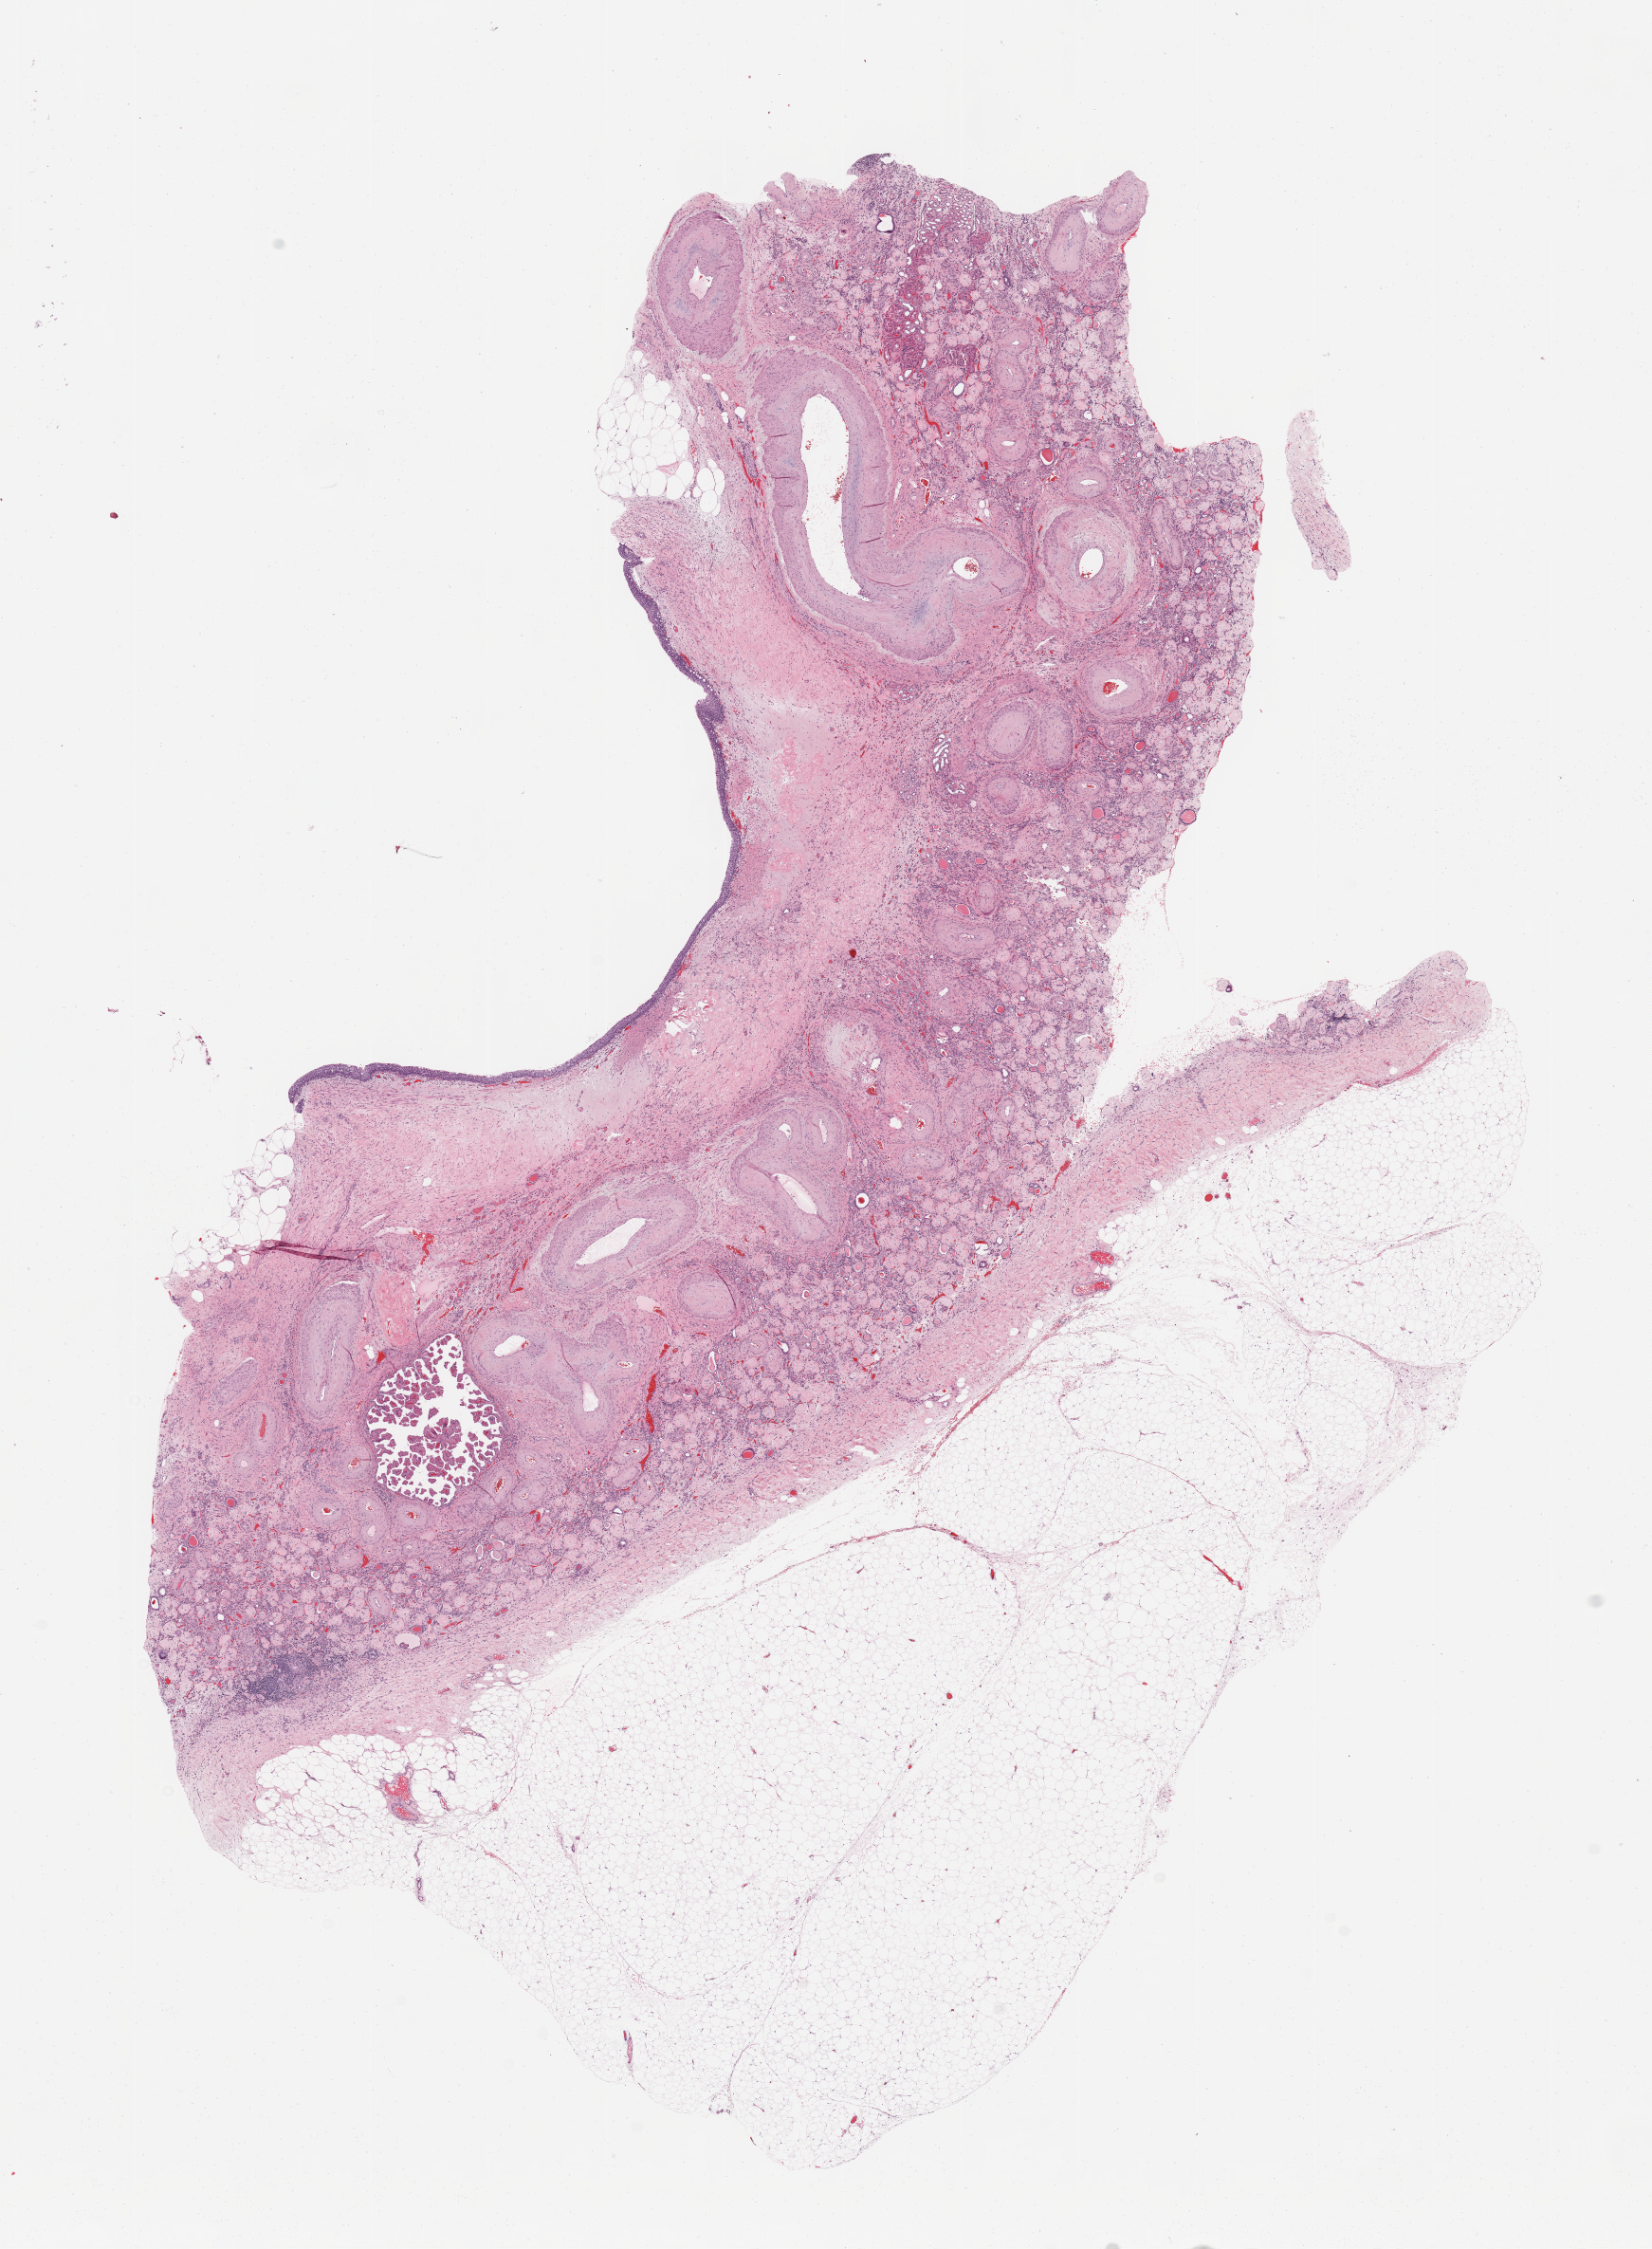
H&E whole-slide image, low-resolution overview of the scanned area, about 13.8 x 18.8 mm (acquisition: 20x scan); kidney, normal (non-tumour) tissue. Patient: female, age 73 years.
This section: normal (non-tumour) tissue from the same patient. Patient diagnosis: Renal cell carcinoma, NOS.